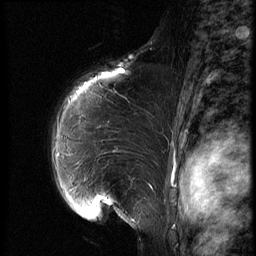
Breast MRI (dynamic contrast-enhanced), one sagittal slice; slice 49 of 66 in the series (ordered by position); dynamic contrast-enhanced series, image 2 of 3 at this slice position (ordered by acquisition); 1.5 T; TE 4.2 ms, TR 8.9 ms; 2.5 mm slice thickness; 256 × 256 image matrix. Patient: female, 39 years. Case-level facts recorded for this patient, not image findings: setting: breast cancer imaged before/during neoadjuvant chemotherapy; receptor status: HER2-positive.
Structures marked on this image (semi-automatic segmentation, software-assisted and operator-edited):
- analysis volume of interest (the breast-tissue region the enhancement analysis was run in; not a lesion): box from (x=47, y=75) to (x=169, y=218) px
- tumour enhancement mask (voxels above the 140 % enhancement threshold inside the analysis volume of interest): (x=89, y=86)–(x=102, y=176)